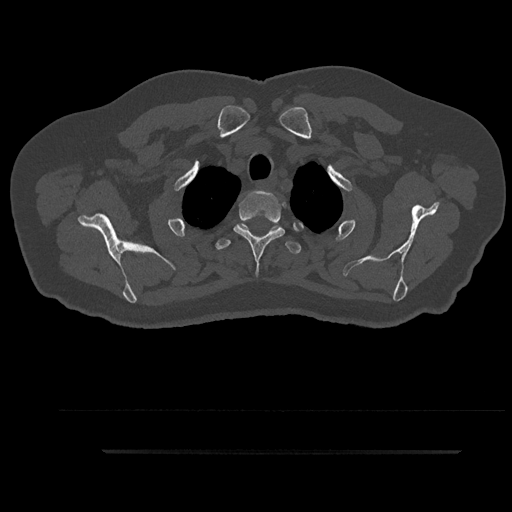
CT including the spine, one axial slice; slice 751 of 797 in the series (ordered by position); bone window (W 1800 / L 400 HU); 0.5 mm slice thickness; 512 × 512 image matrix, field of view 432 × 432 mm. Male patient, age 63 years. From the clinical record (not read from this slice): primary cancer: renal; vertebrae with lytic lesions (as recorded): T8.
Outlined on this slice (semi-automatic segmentation, software-assisted and operator-edited):
- T2 vertebra: bounding box <234,191,303,275> (left, top, right, bottom; pixels)
- T3 vertebra: <215,223,301,255>